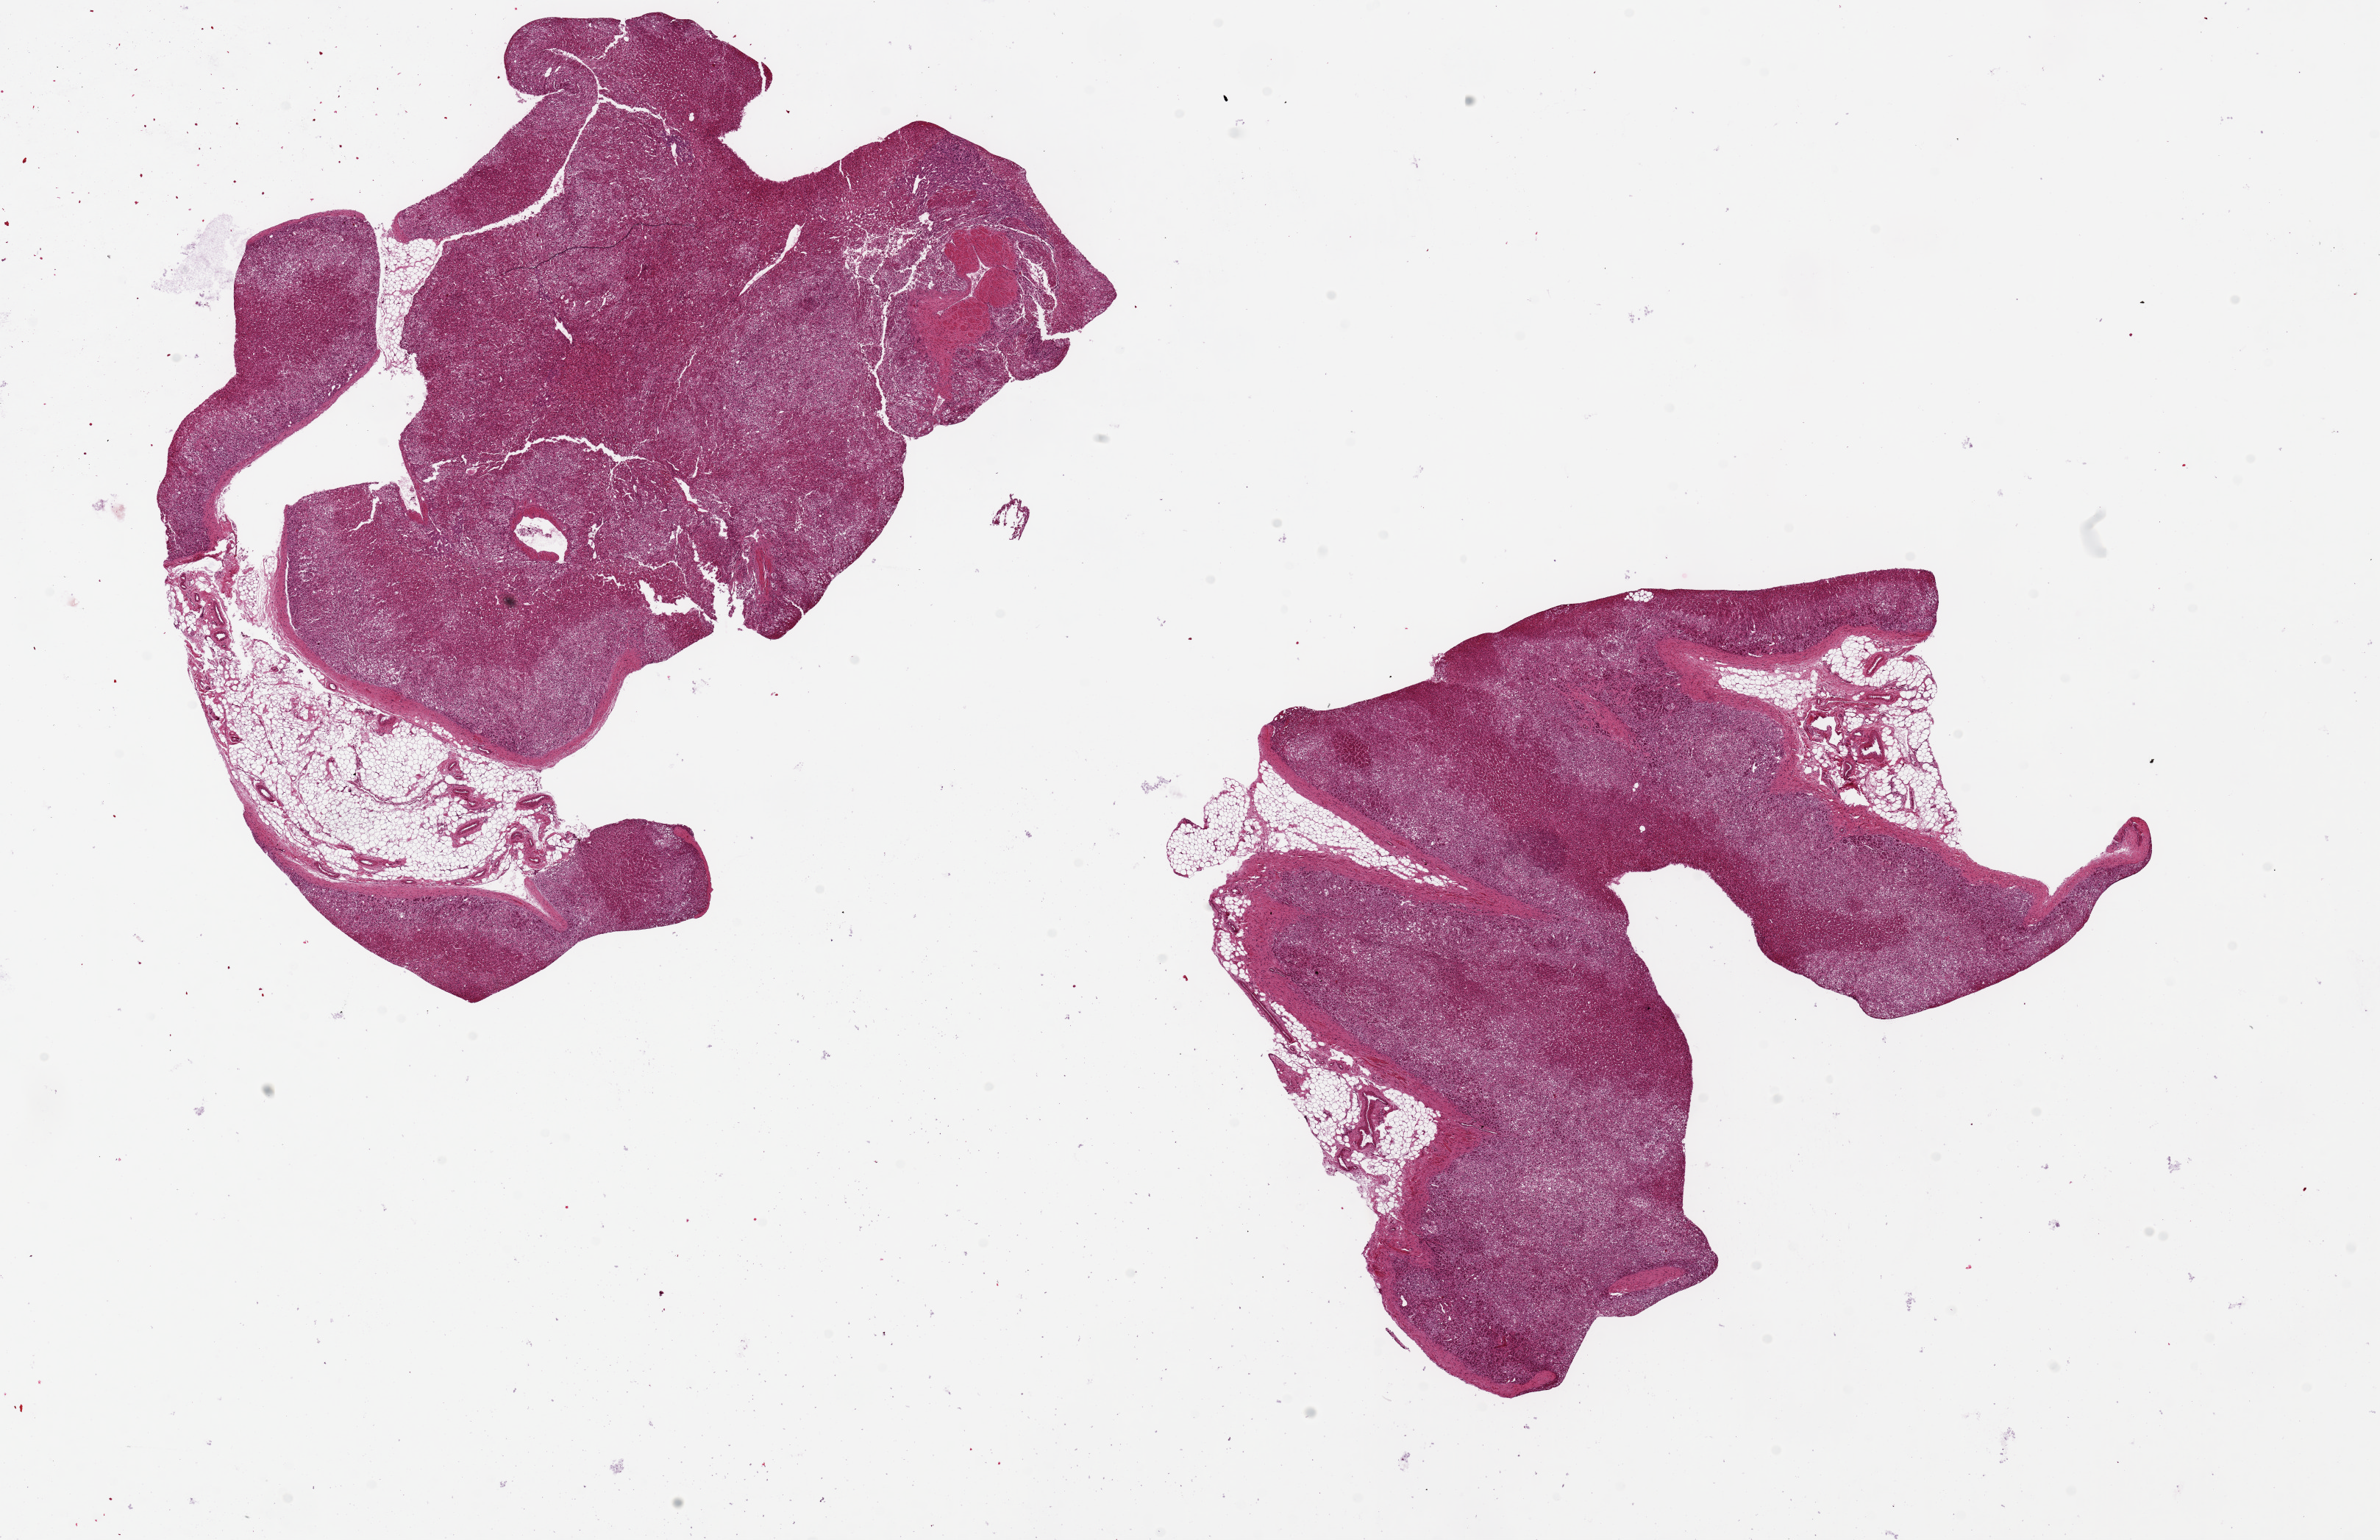
Digitized haematoxylin and eosin-stained section — shown as a low-resolution overview of the whole scanned area (about 25.6 x 16.6 mm). PAXgene-fixed, paraffin-embedded tissue. Target tissue: adrenal gland. Donor tissue sample. Donor: male.
• review note (as recorded): 2 pieces ~8x8mm, all cortex, well preserved; A few 1-2 mm foci of partially interstitial fat